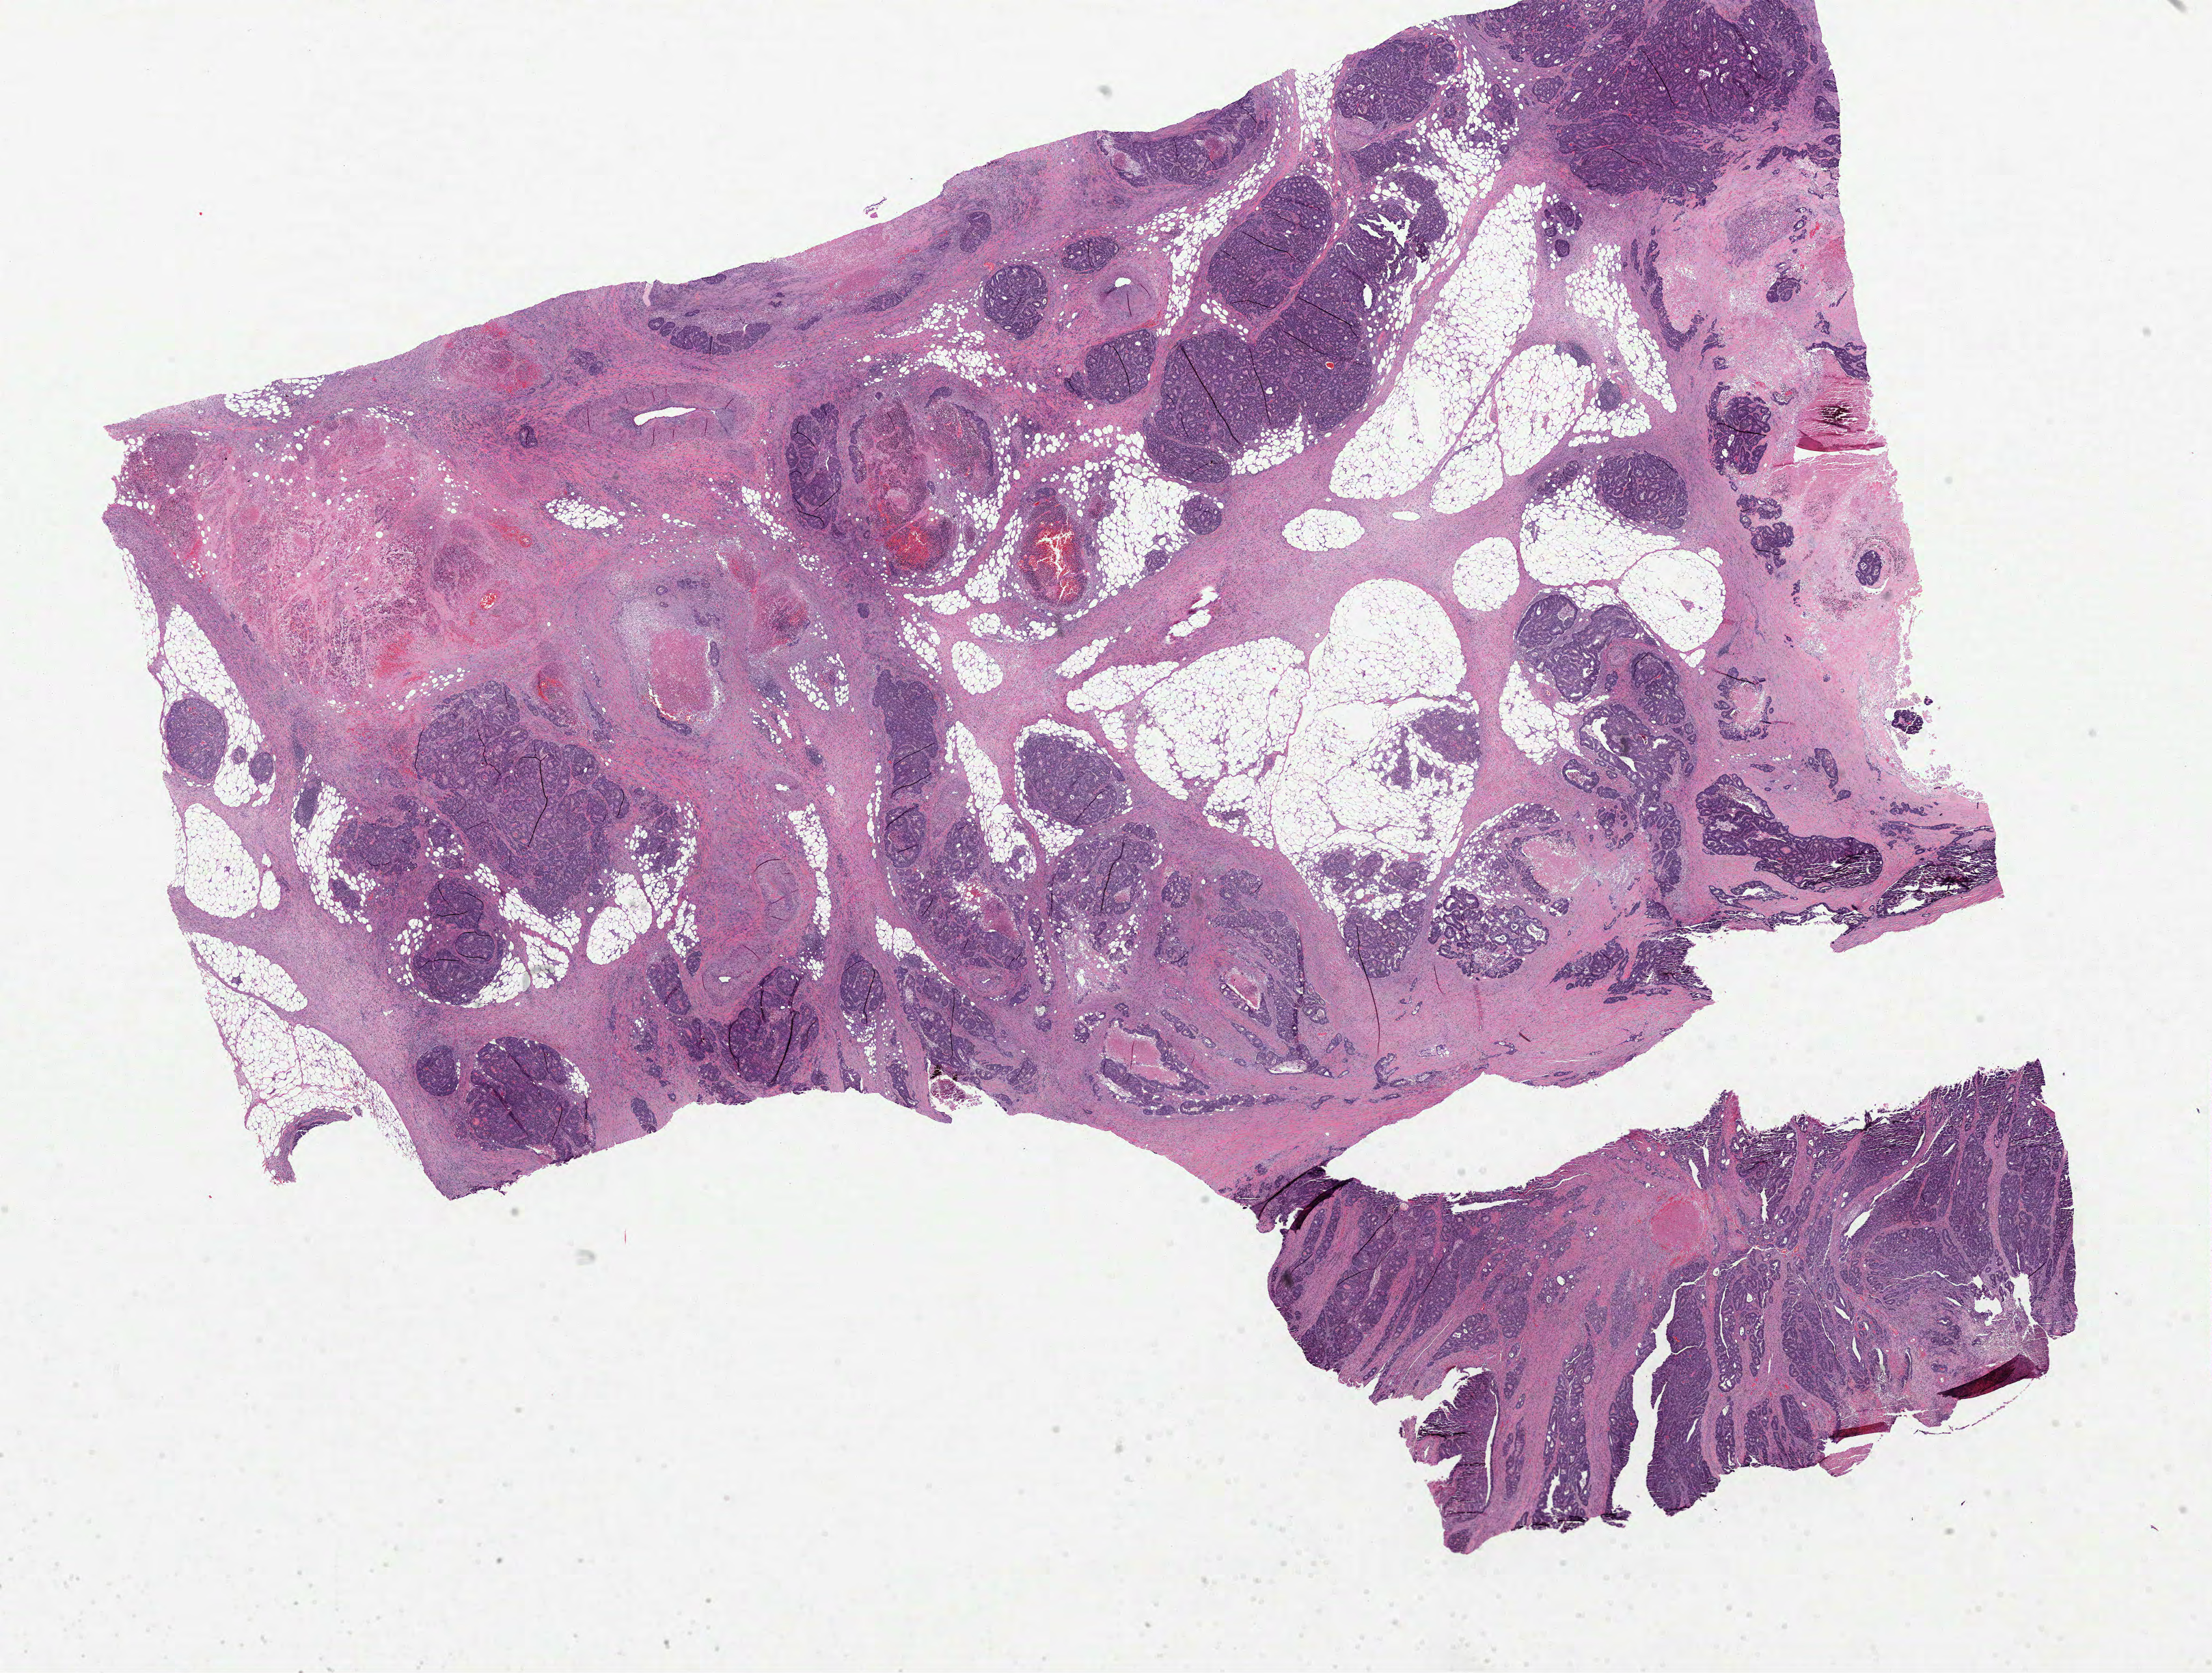
Whole-slide histology image, H&E-stained, shown as a low-resolution overview of the whole scanned area (about 26.1 x 19.7 mm, slide scanned at 40x); FFPE section; sample: primary tumour, colon. Male, age 80 years at initial diagnosis.
Pathologic diagnosis: Adenocarcinoma, NOS (ascending colon).